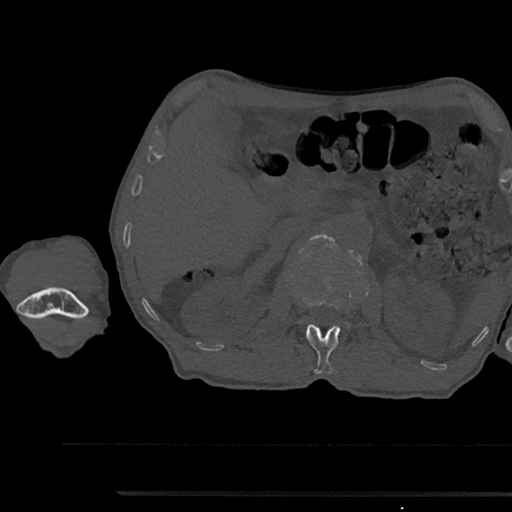
CT including the spine, one axial slice. Position 614 of 797 along the scan axis. Reconstruction kernel Br40s/3. 120 kVp. Bone window (W 1800 / L 400 HU). 512 × 512 image matrix, field of view 367 × 367 mm. Male patient, age 79 years. Case-level facts recorded for this patient, not image findings: primary cancer: prostate.
Outlined on this slice (semi-automatically segmented with operator editing):
- L1 vertebra: bounding box <295,296,340,374> (left, top, right, bottom; pixels)
- L2 vertebra: <308,234,335,305>